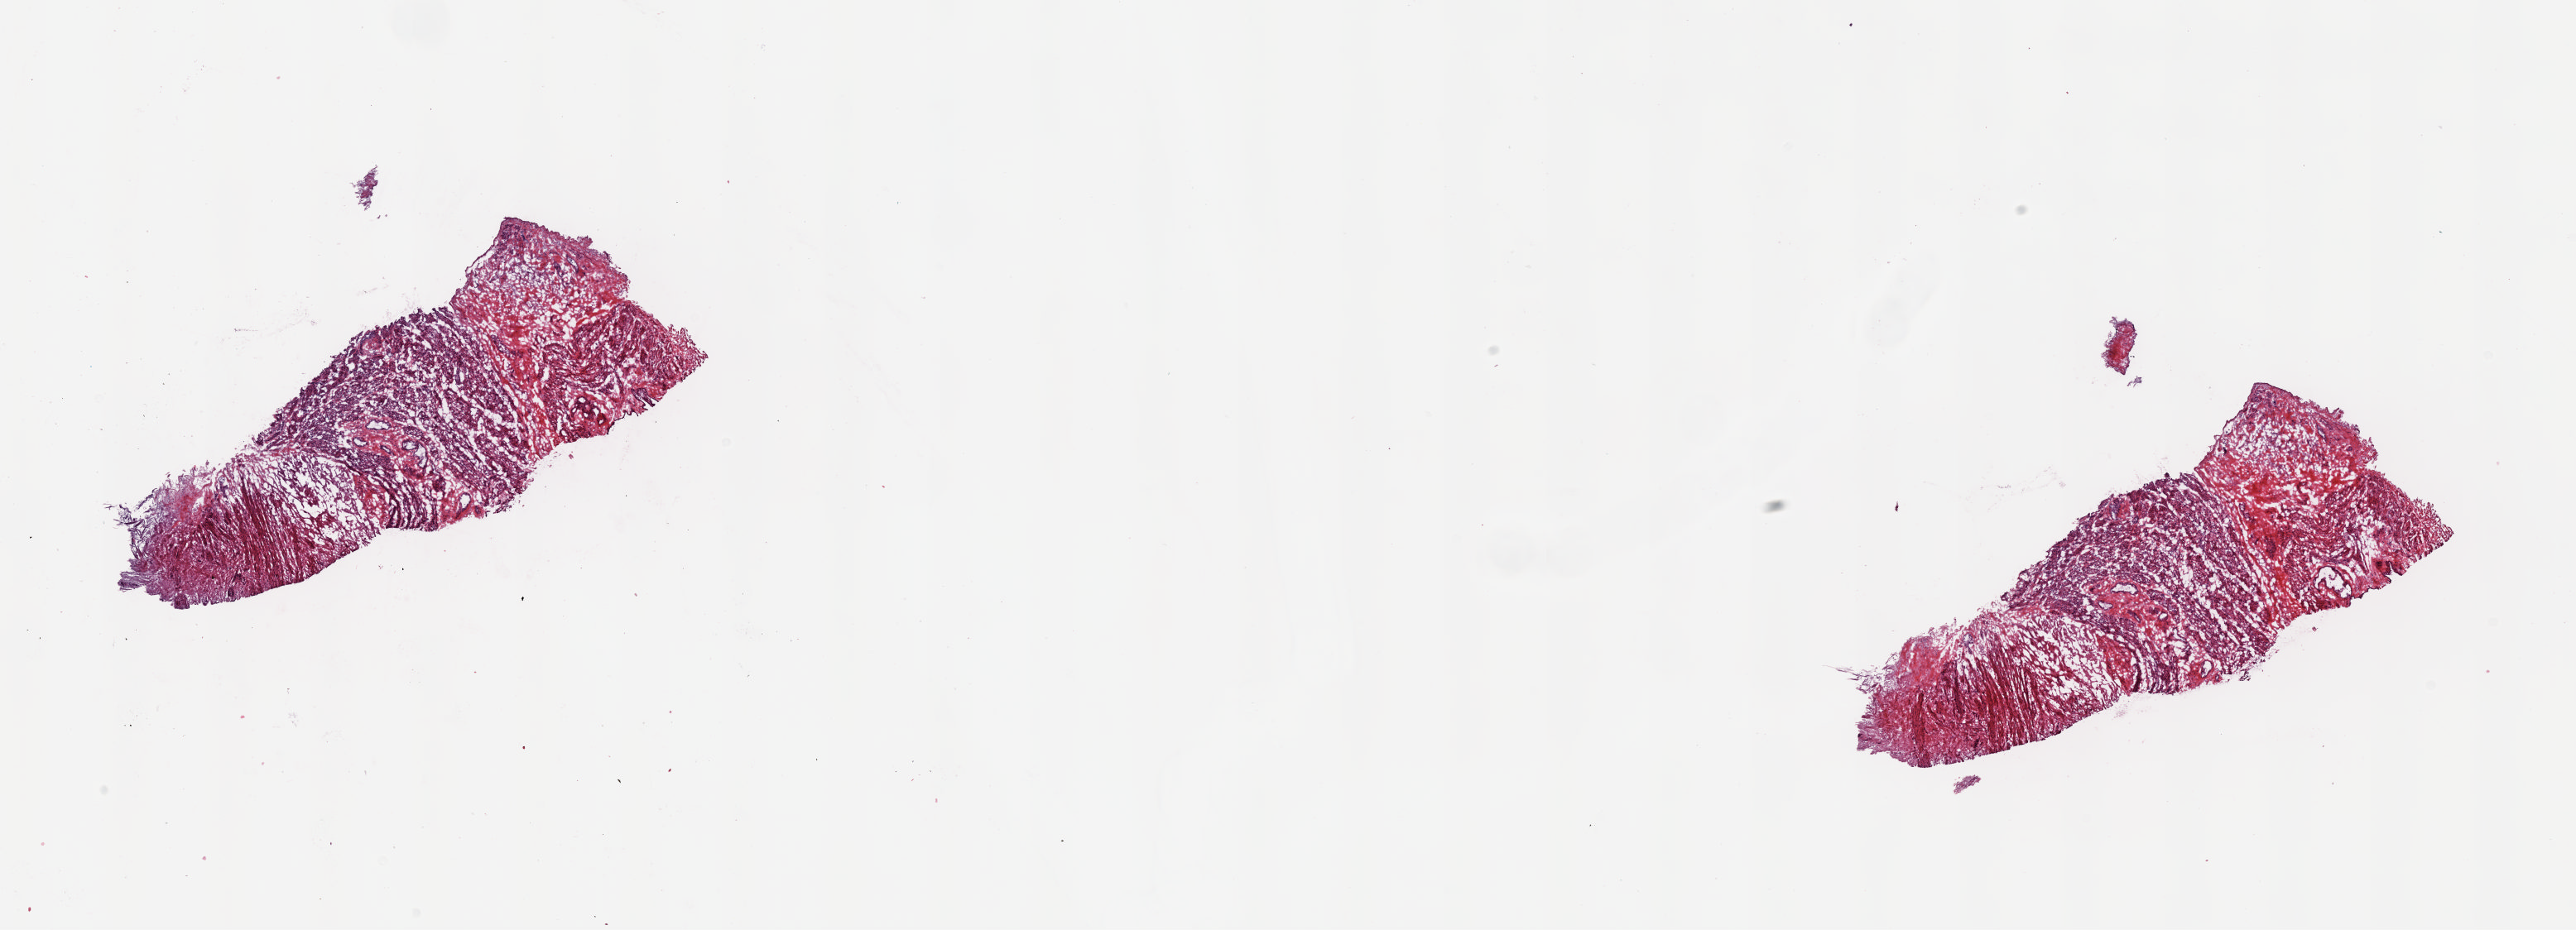
Digitized H&E-stained tissue section (whole slide) — low-resolution overview of the scanned area, about 24.6 x 8.9 mm. Frozen section from the top of the tissue portion. Sample: solid tissue normal (non-tumour tissue), uterus. Patient: female, age at initial diagnosis 67 years. Pathologist review of this section (percent, as recorded): tumour cells 0%, tumour nuclei 0%, normal cells 100%, stromal cells 0%, necrosis 0%. Inflammatory infiltration, as recorded: lymphocyte infiltration 0%, monocyte infiltration 0%, neutrophil infiltration 0%.
This section: solid tissue normal sample (biorepository sample class). Patient diagnosis: Serous cystadenocarcinoma, NOS (endometrium).